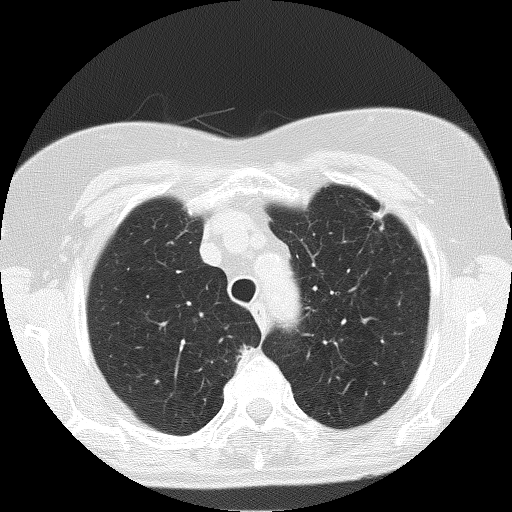
Low-dose screening chest CT, one axial slice. Slice 136 of 166 in the series (ordered by position). Reconstruction kernel FC51. 120 kVp. Lung window (W 1500 / L -600 HU). 2 mm slice thickness. 512 × 512 image matrix, field of view 303 × 303 mm.
Outlined on this slice (expert manual segmentation):
- lesion 1 (tumor, upper lobe of left lung): bounding box <373,211,384,220> (left, top, right, bottom; pixels)